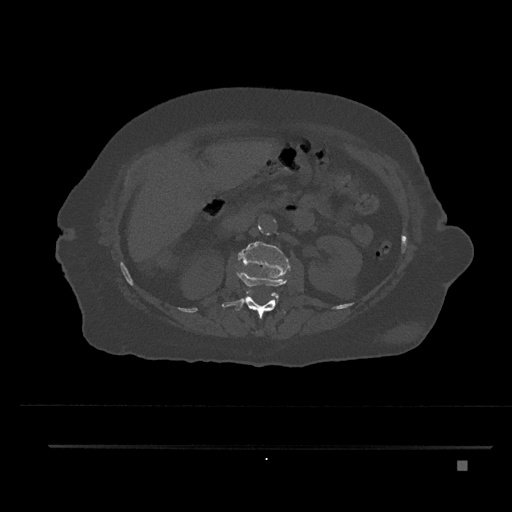
CT including the spine, one axial slice; position 209 of 797 along the scan axis; reconstruction kernel Br40s/3; 120 kVp; bone window (W 1800 / L 400 HU); 0.5 mm slice thickness; 512 × 512 image matrix, field of view 437 × 437 mm. Female patient, age 76 years. Case-level facts recorded for this patient, not image findings: primary cancer: lung.
Outlined on this slice (semi-automatically segmented with operator editing):
- L1 vertebra: bounding box (x1, y1, x2, y2) in pixels: (222, 271, 288, 319)
- L2 vertebra: (238, 241, 291, 298)